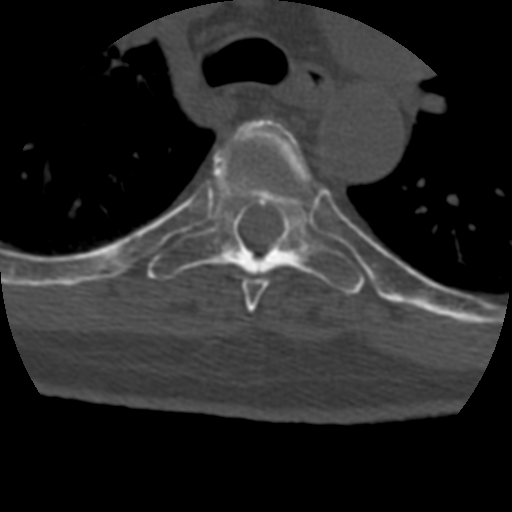
CT including the spine, one axial slice. Slice 308 of 399 in the series (ordered by position). 120 kVp. Bone window (W 1800 / L 400 HU). 512 × 512 image matrix. Patient age 69 years. Case-level facts recorded for this patient, not image findings: primary cancer: prostate.
Outlined on this slice (semi-automatic segmentation, software-assisted and operator-edited):
- T5 vertebra: bounding box <232,119,309,313> (left, top, right, bottom; pixels)
- T6 vertebra: <147,148,365,295>